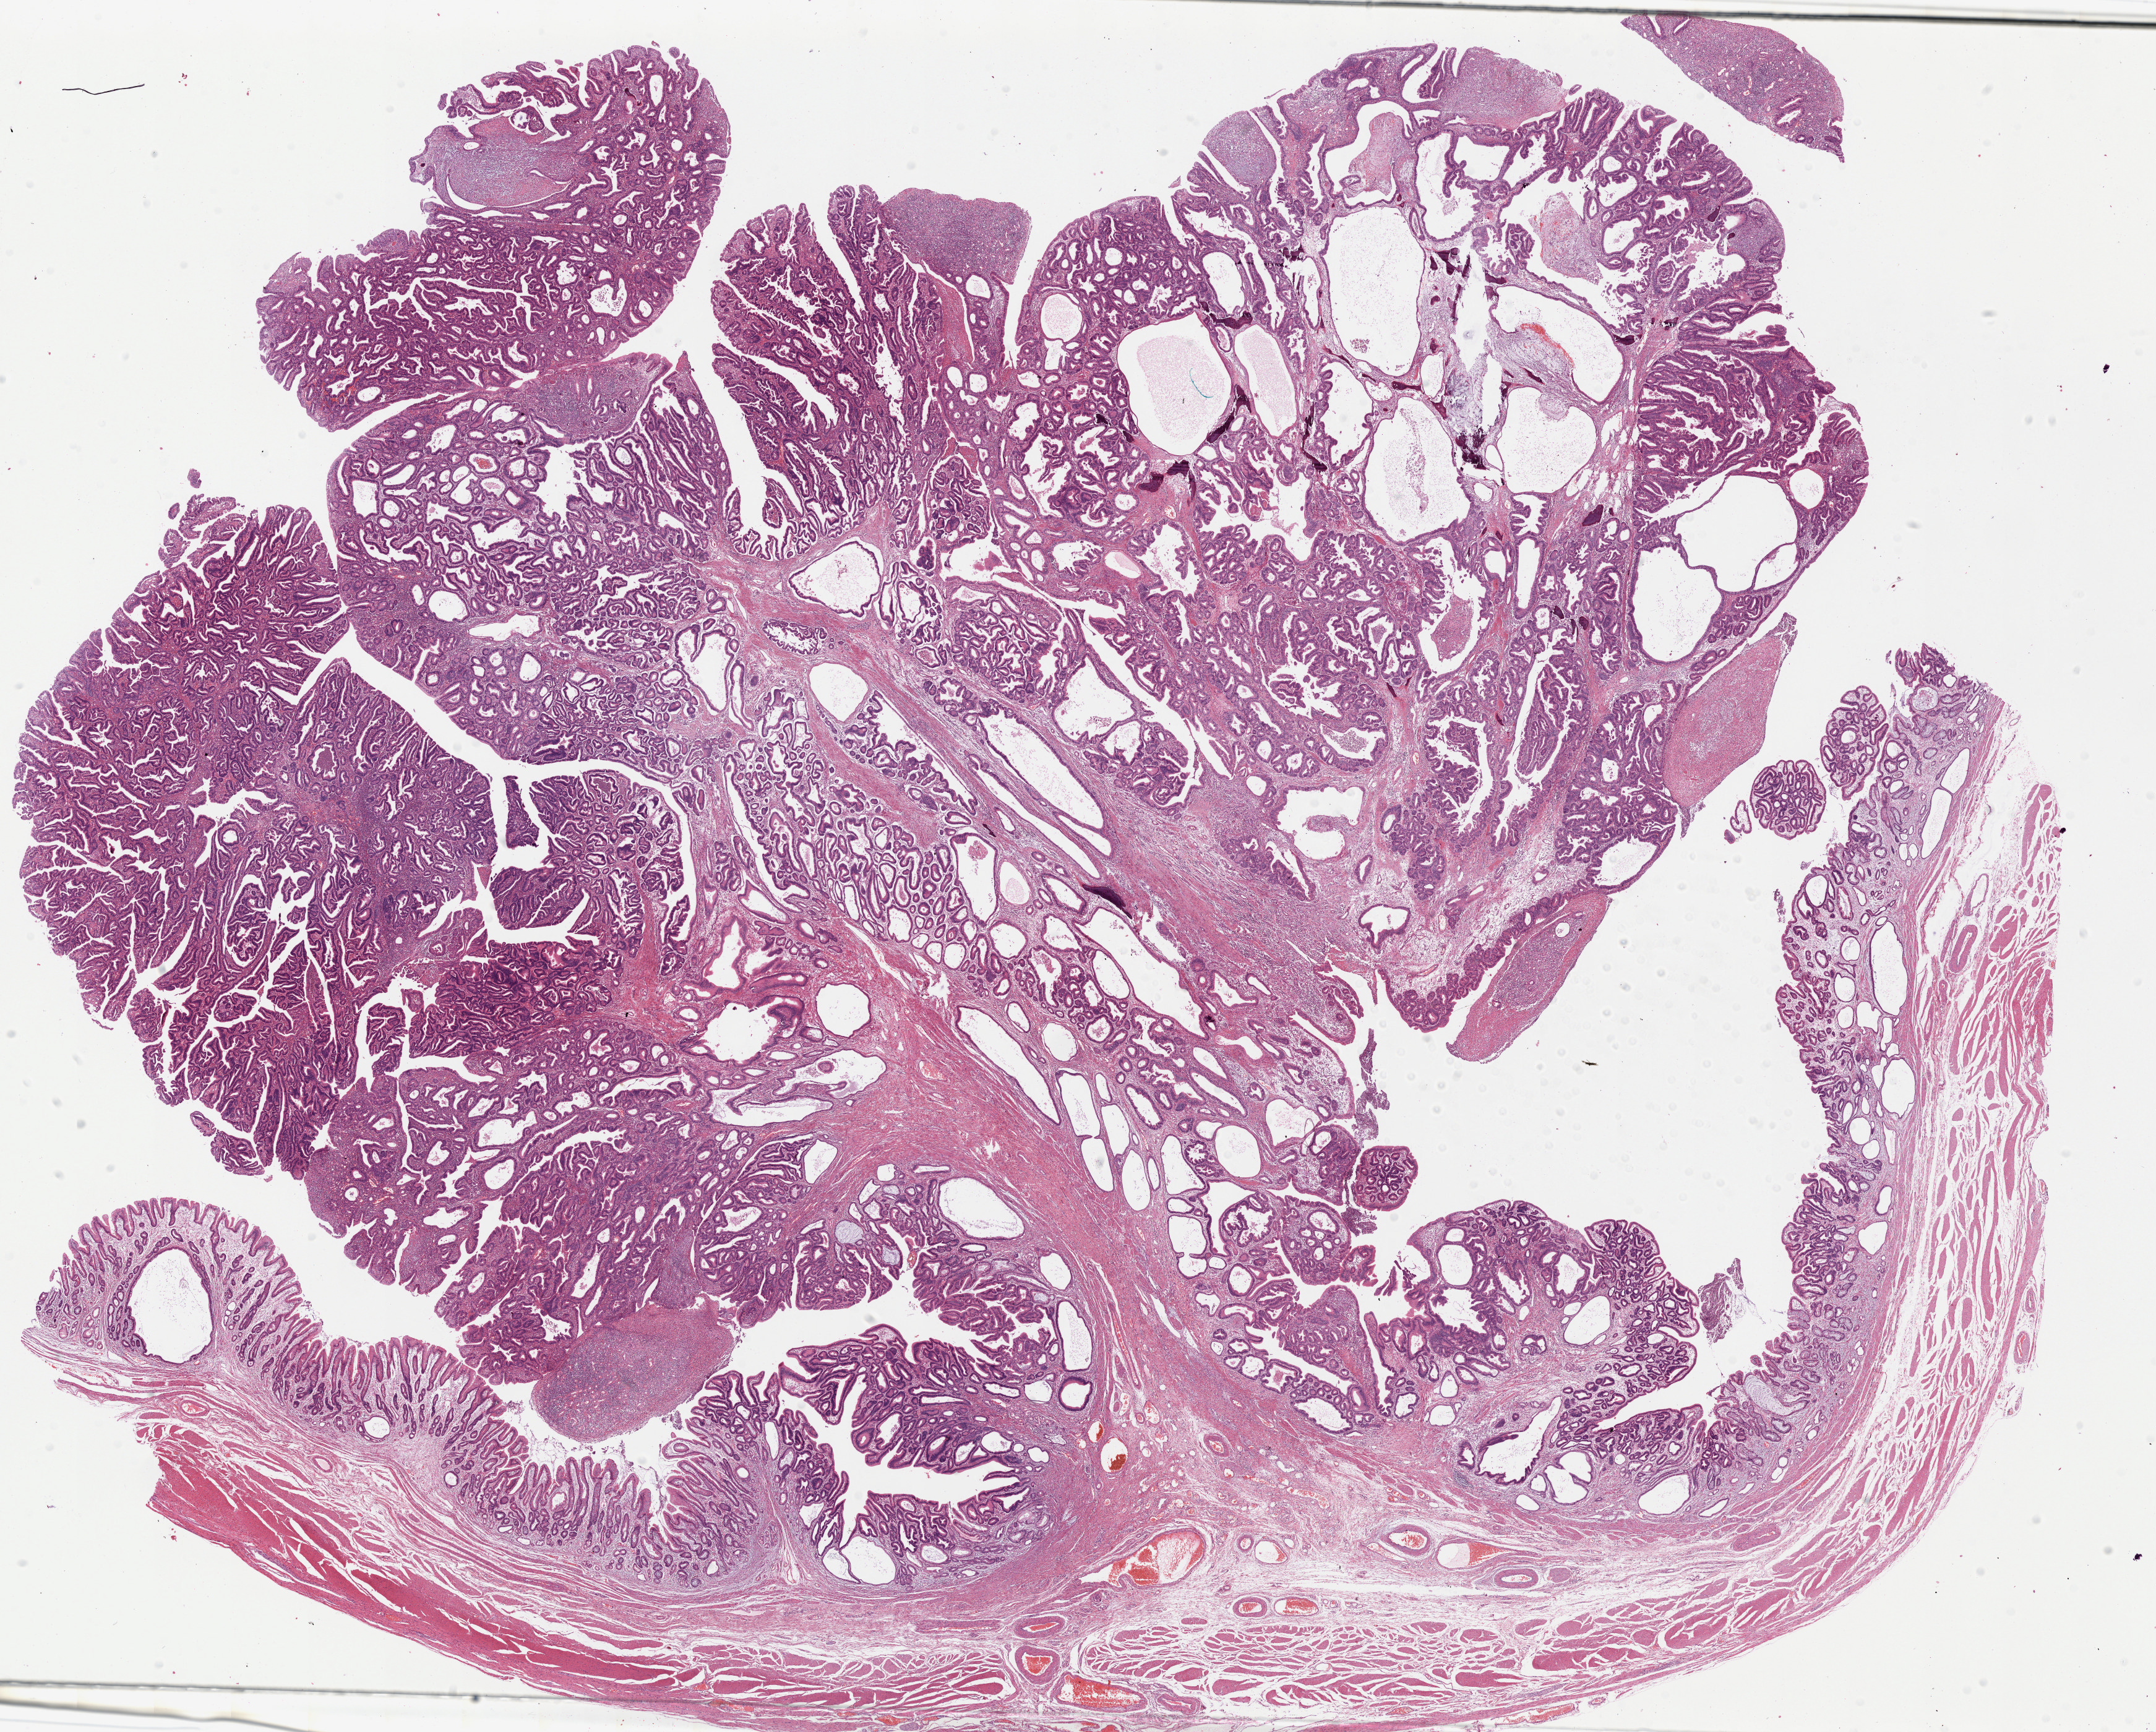
H&E-stained whole-slide image, low-resolution overview of the scanned area, about 27.6 x 22.2 mm (acquisition: 20x scan); formalin-fixed paraffin-embedded (FFPE) diagnostic section; sample: primary tumour, stomach. Female patient; age at initial diagnosis 77 years. Histologic grade: G1 (well differentiated).
* lymph nodes positive (case pathology): 0 of 32 examined
* AJCC pathologic stage: IA (7th edition)
* pathologic diagnosis: Tubular adenocarcinoma (body of stomach)